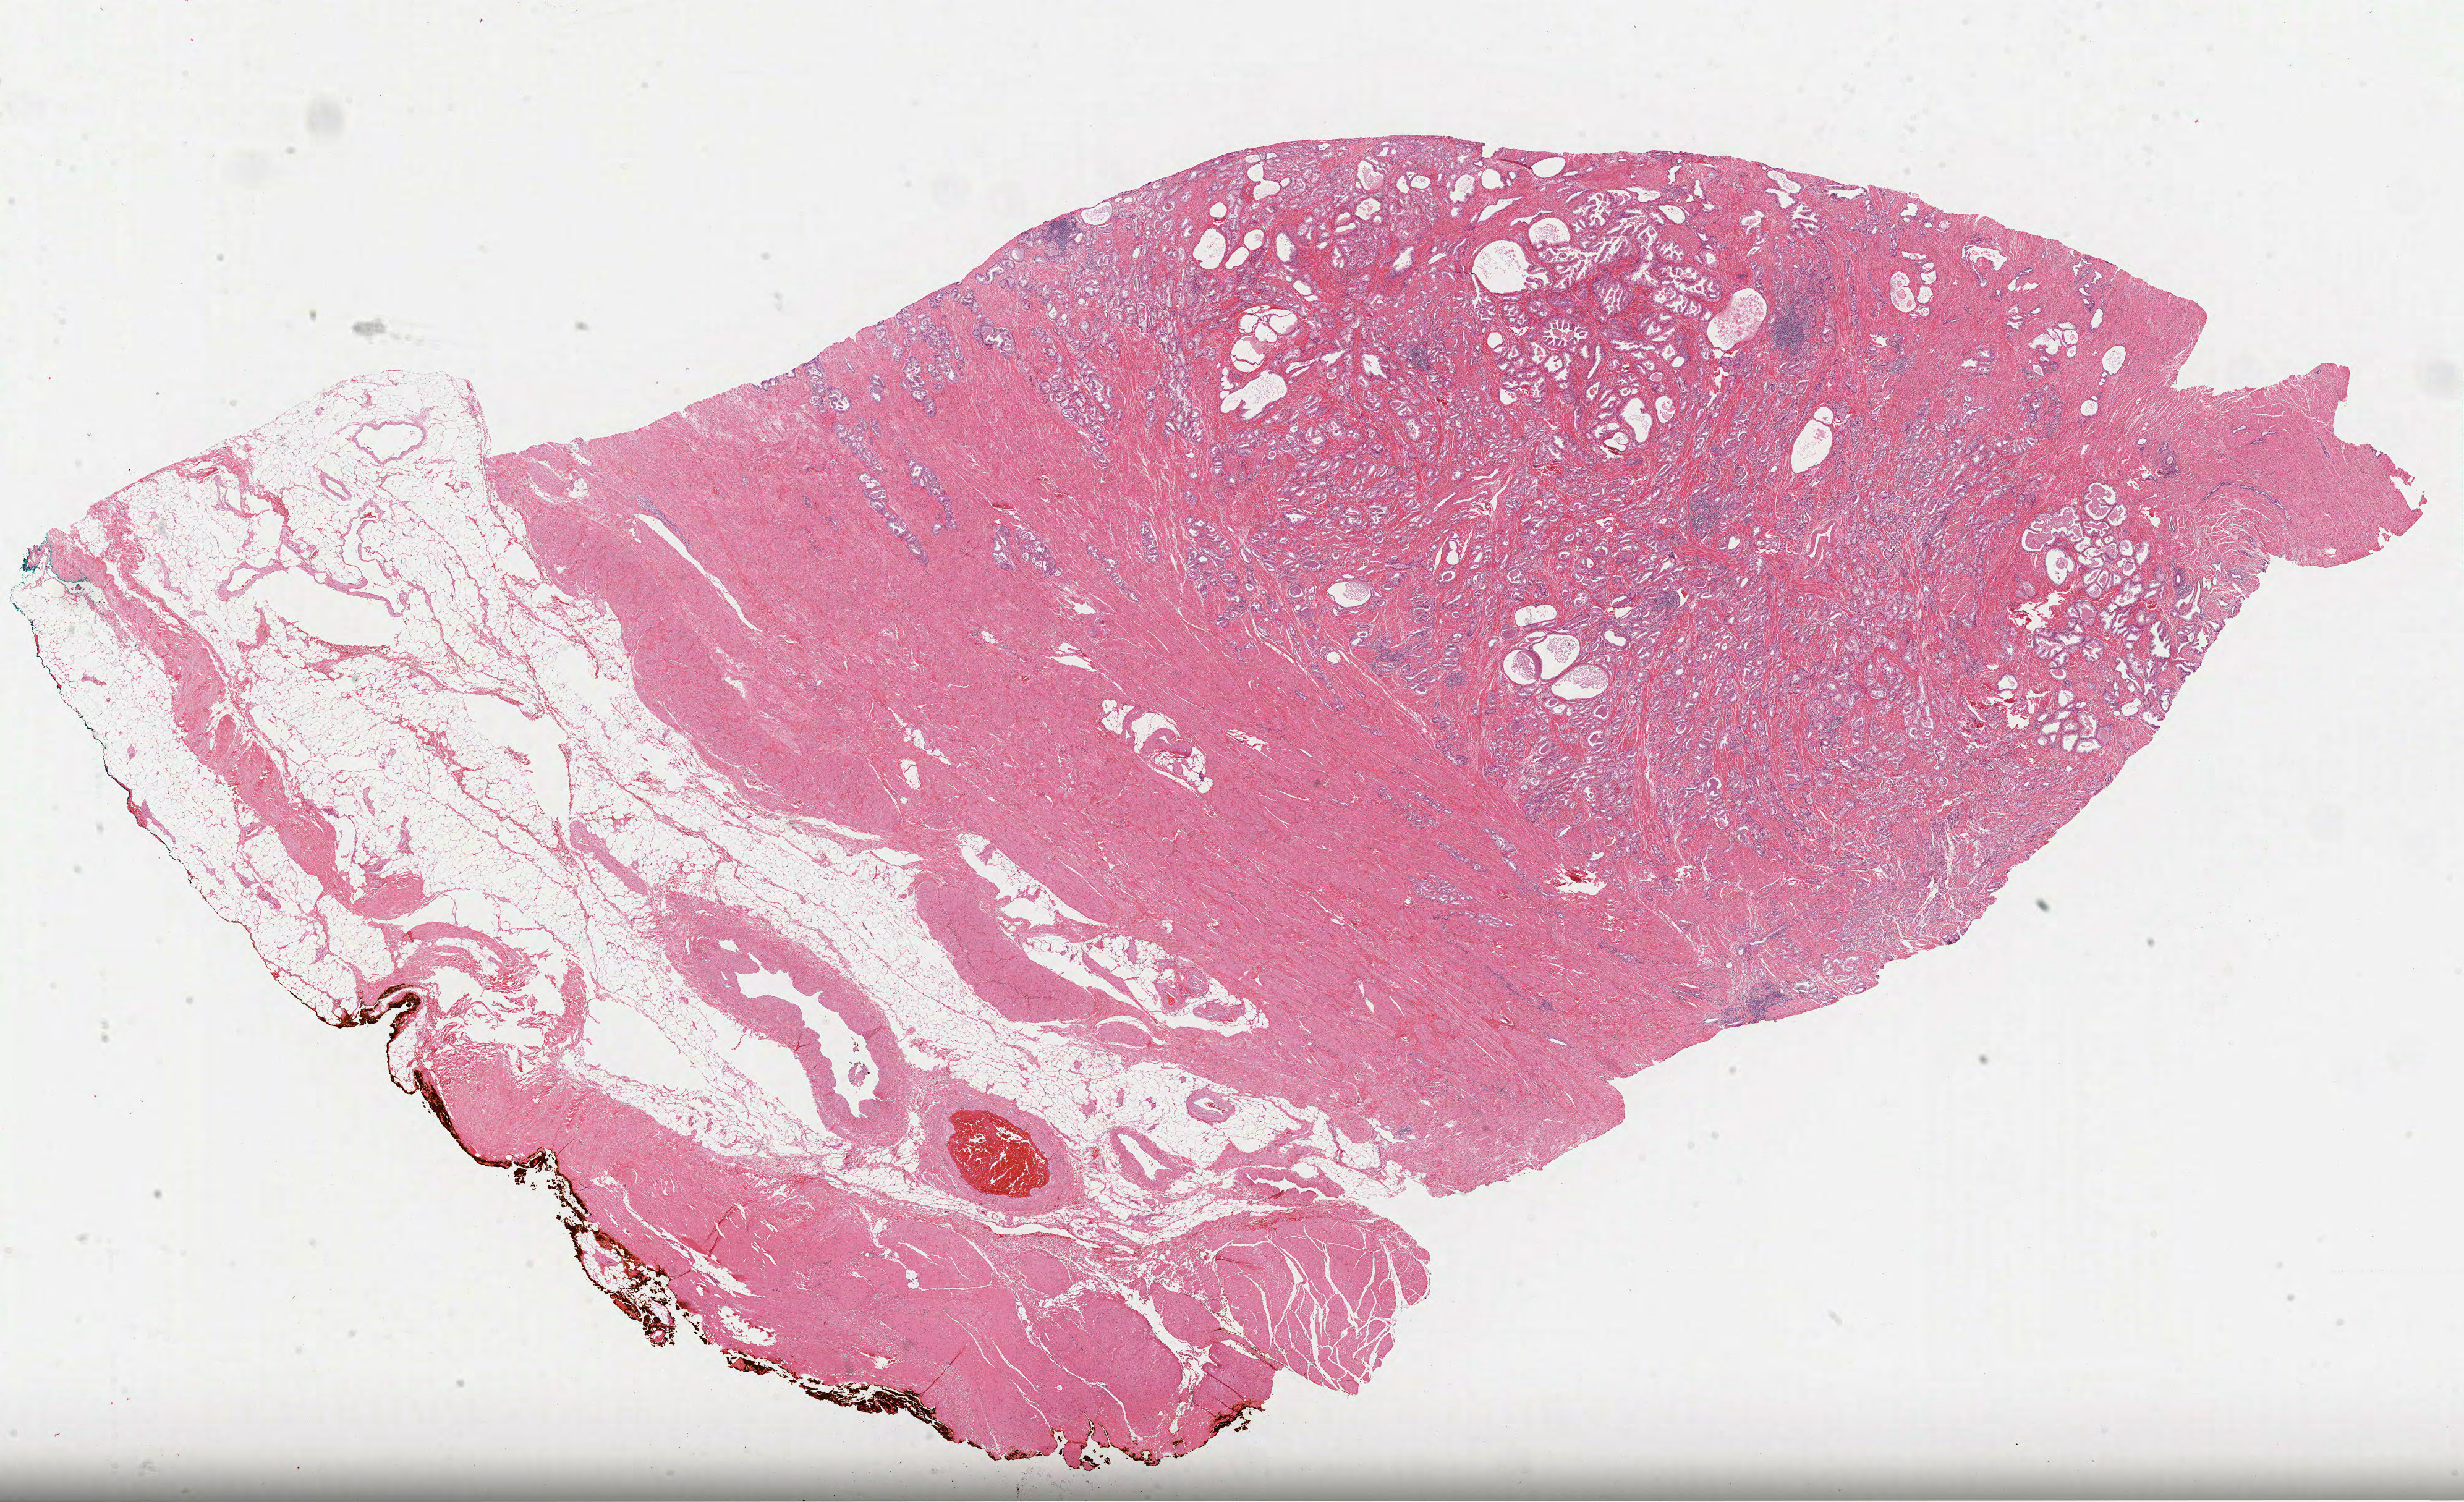
Whole-slide histology image, H&E-stained, whole scanned area (about 32.1 x 19.6 mm, from a 40x scan) shown as a low-resolution overview, FFPE section, sample: primary tumour, prostate. Patient: male, age at initial diagnosis 52 years. Gleason score: 7 (3+4).
- histologic diagnosis: Acinar cell carcinoma (prostate gland)